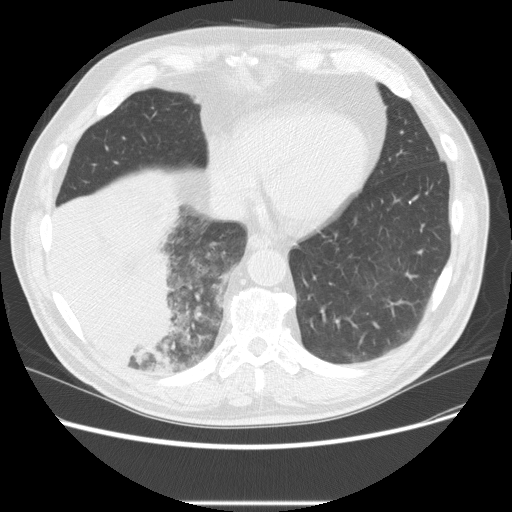
Low-dose screening chest CT, one axial slice. Position 66 of 233 along the scan axis. Reconstruction kernel STANDARD. 120 kVp. Lung window (W 1500 / L -600 HU). 2.5 mm slice thickness. 512 × 512 image matrix, field of view 380 × 380 mm.
Structures marked on this image (outlined manually by an expert reader):
- lesion 3 (tumor, lower lobe of right lung): box from (x=51, y=196) to (x=177, y=365) px